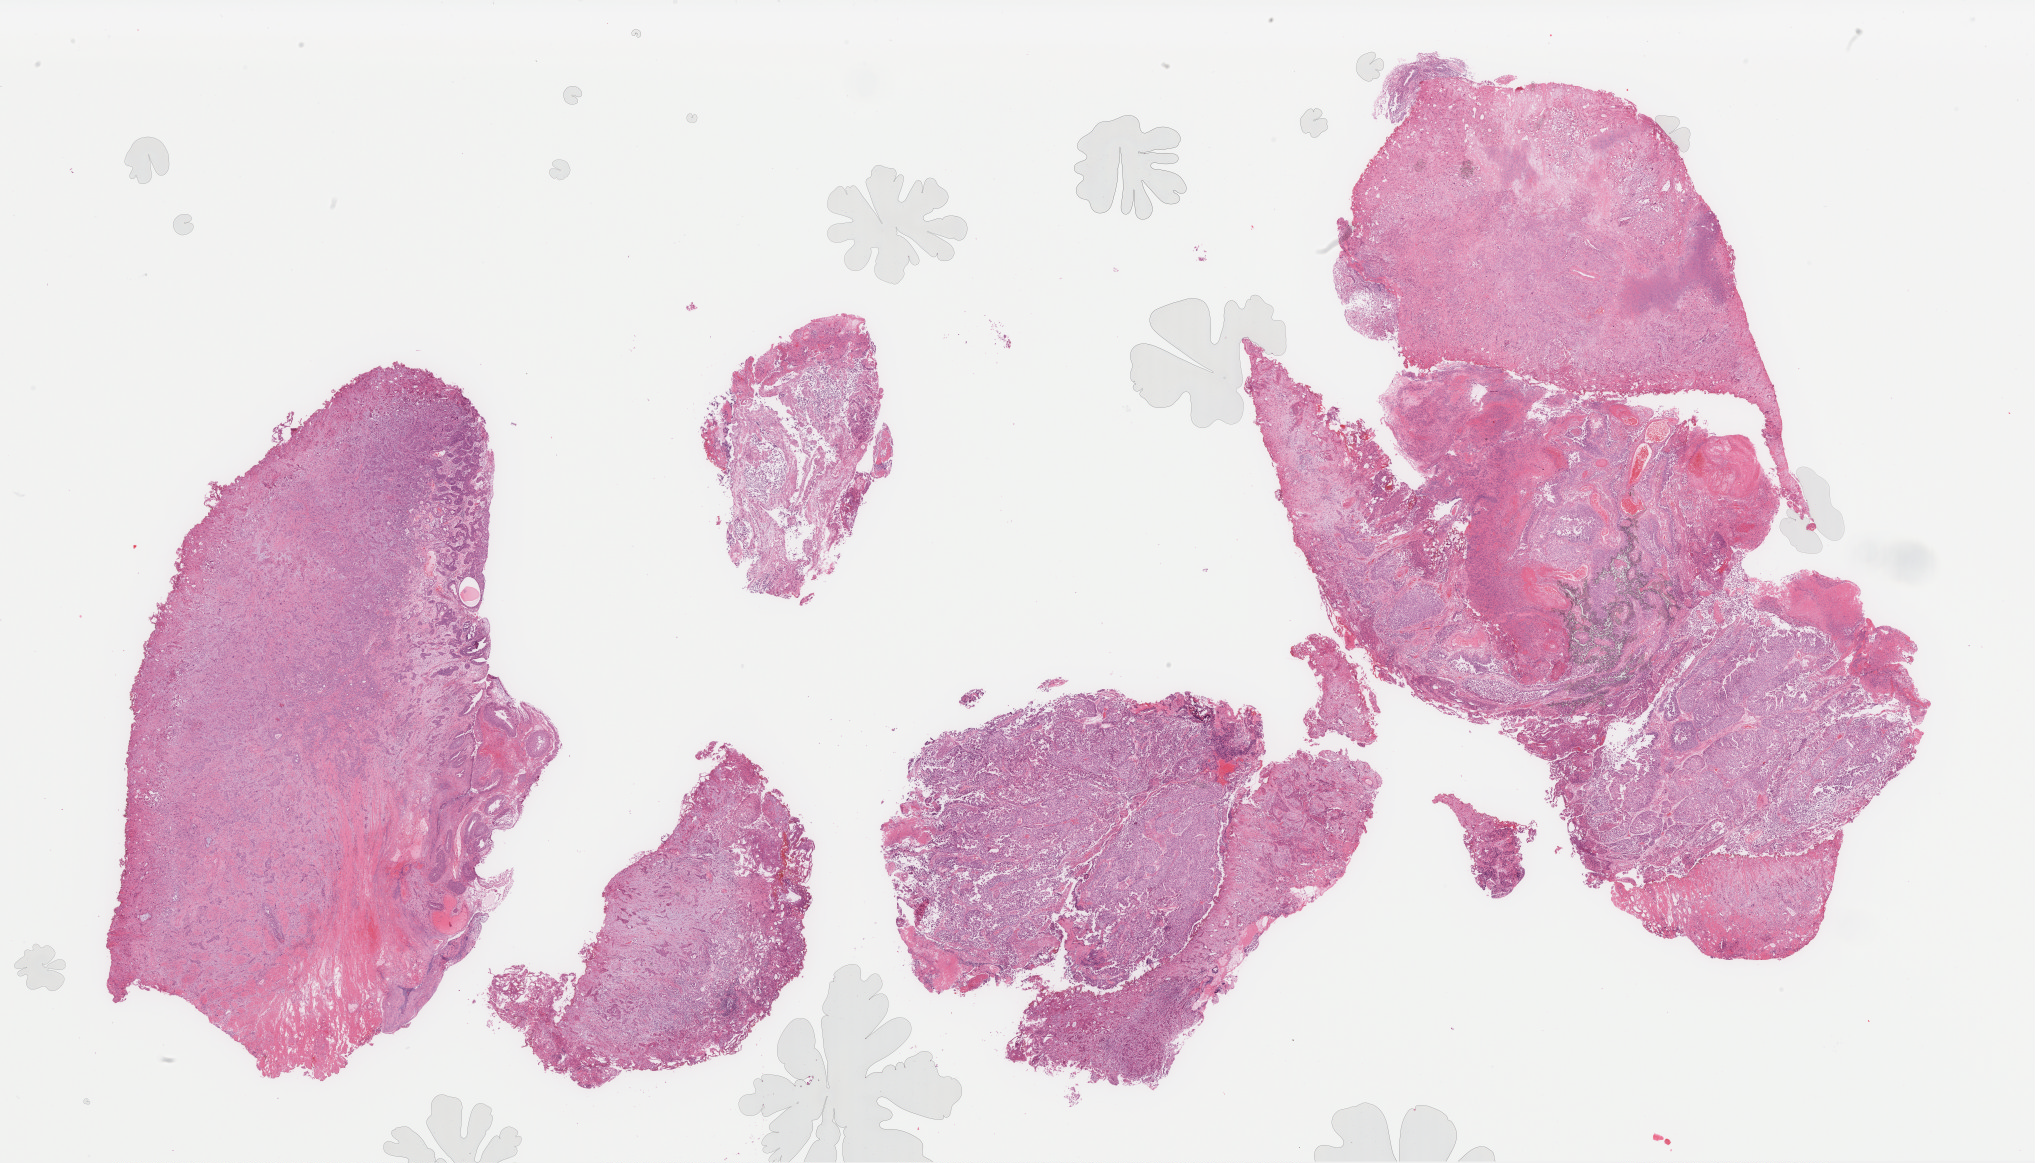
Whole-slide histology image, H&E-stained — a low-resolution overview of the entire scanned area, about 32.3 x 18.5 mm (acquisition: 40x scan). Formalin-fixed paraffin-embedded (FFPE) diagnostic section. Bladder, primary tumour sample. Patient: male, age at initial diagnosis 67 years. Histologic grade: high grade.
* TNM: NX MX
* AJCC pathologic stage: II (7th edition)
* diagnosis: Transitional cell carcinoma (trigone of bladder)